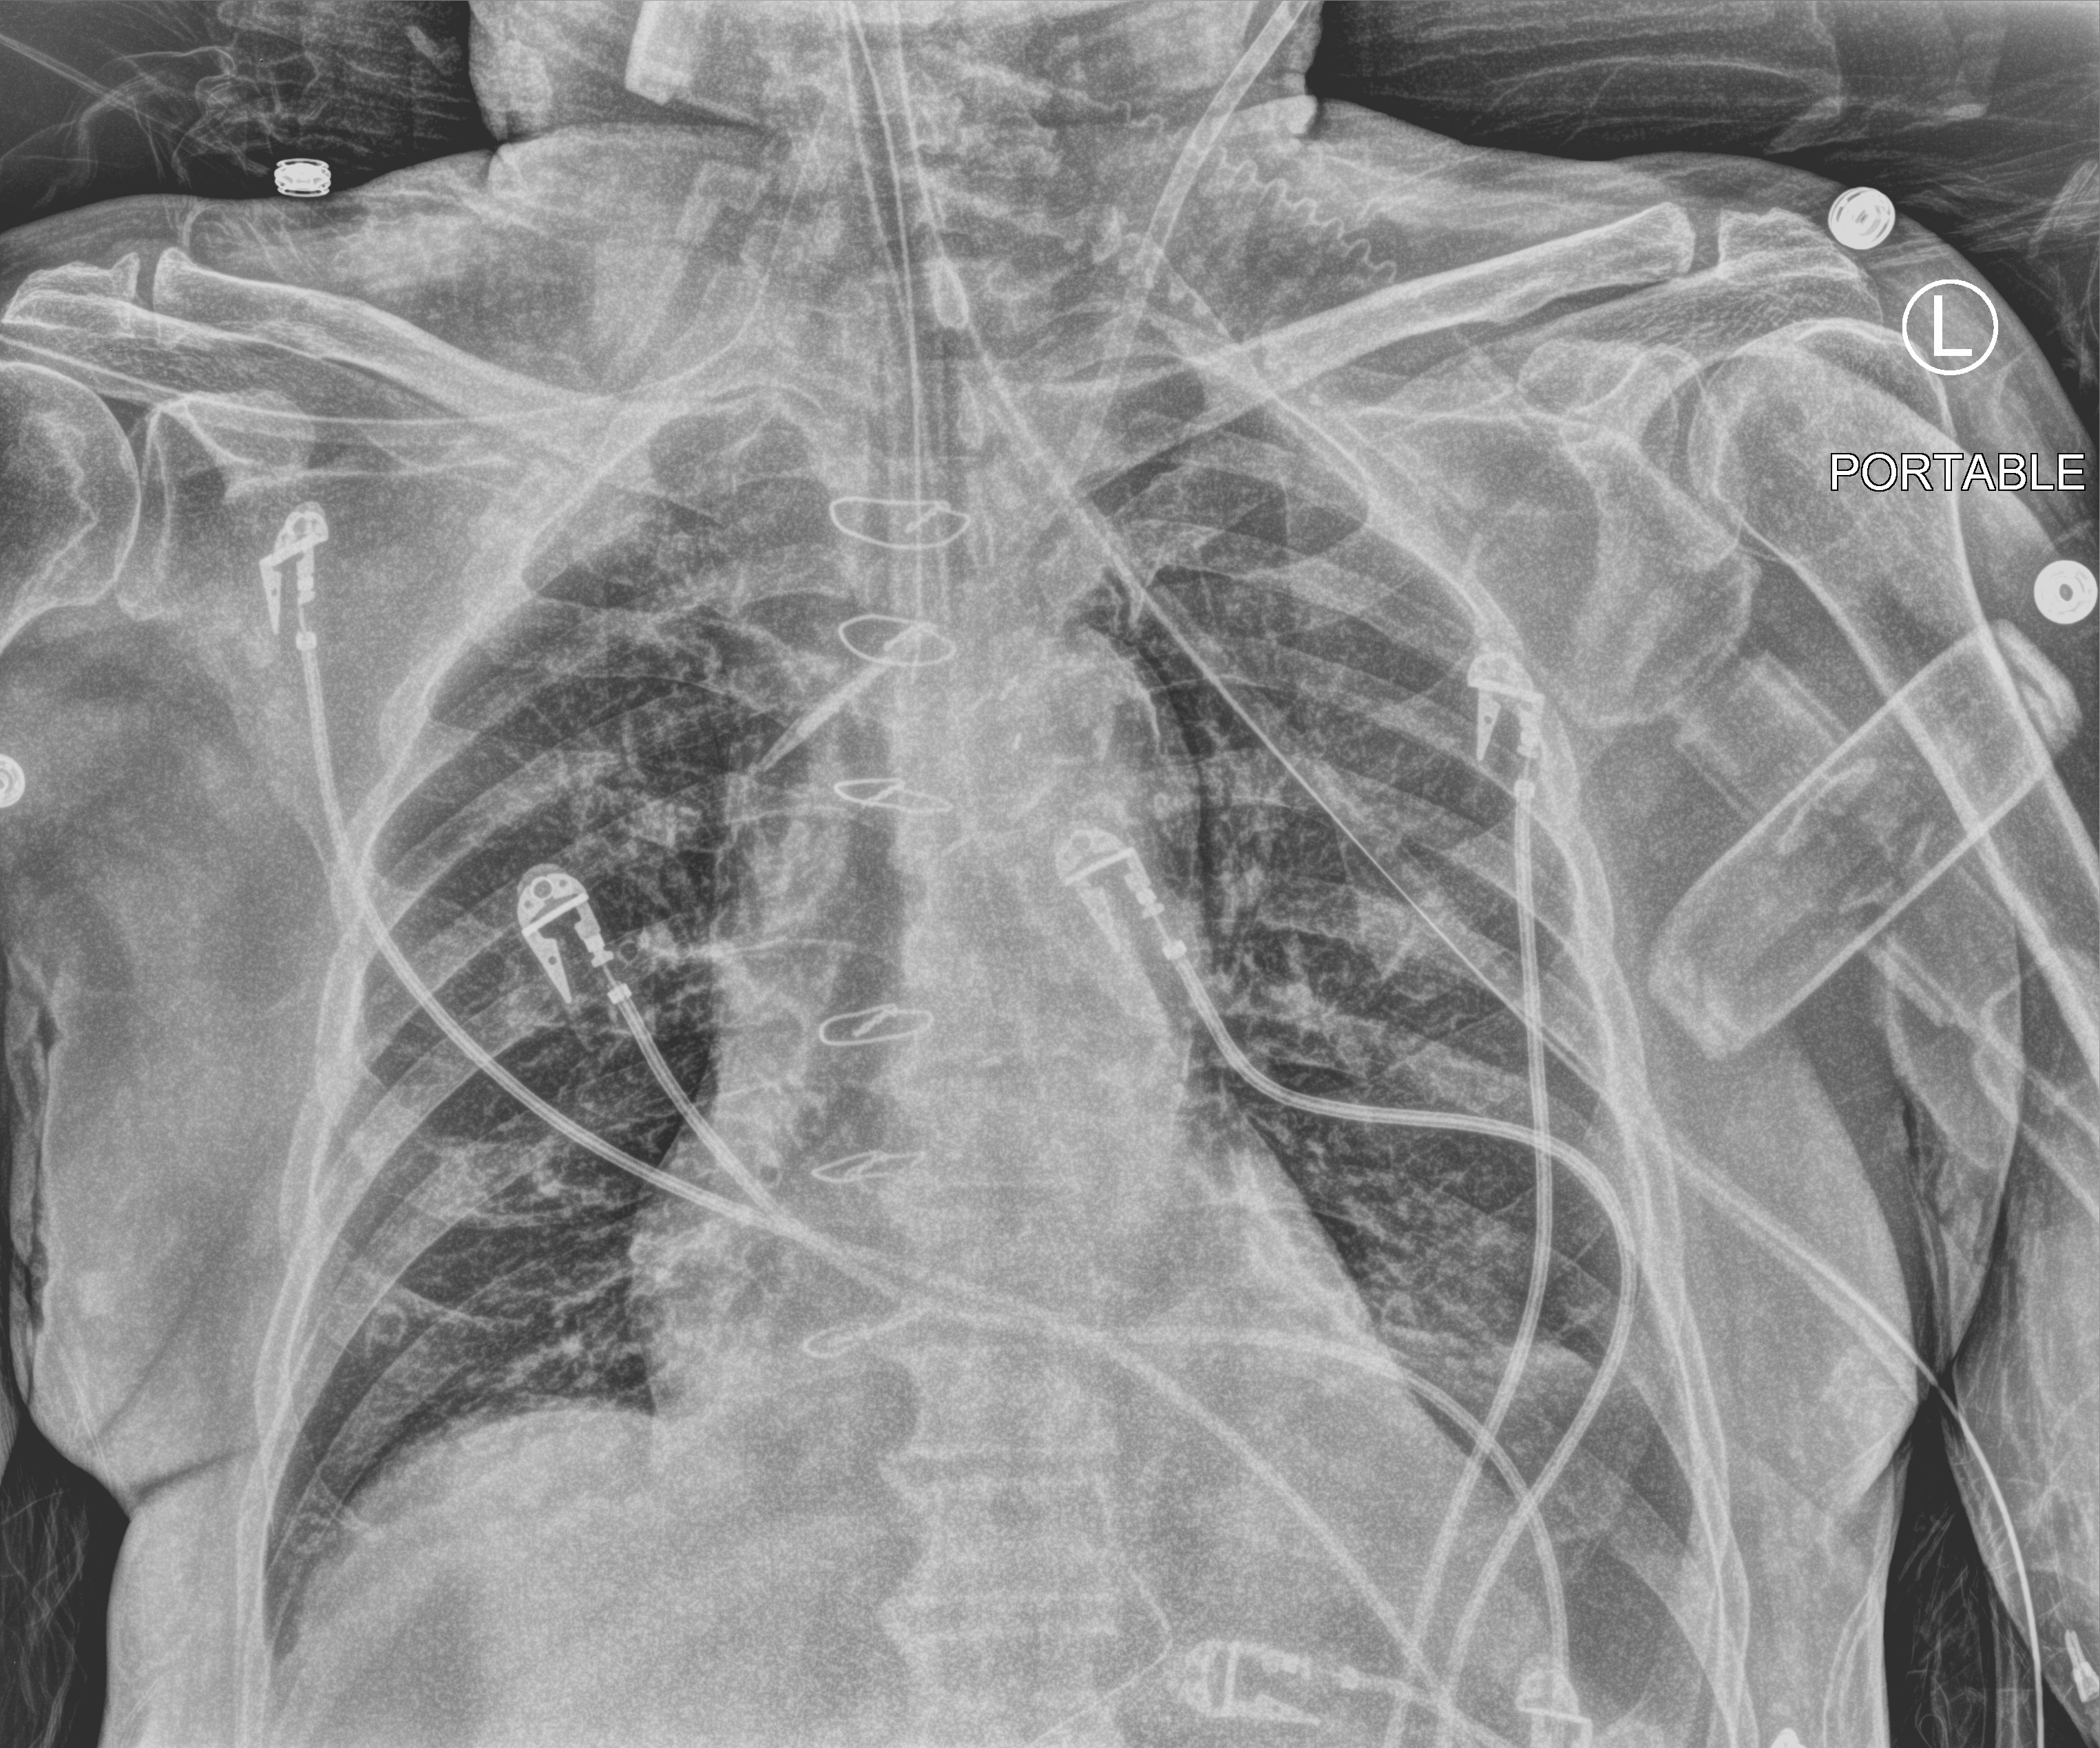
Bedside chest radiograph (computed radiography). Patient hospitalised with COVID-19; male, aged 75–90 years.
Hospital-stay facts (about this admission, not read from this image; timing relative to this image not recorded):
- mechanically ventilated during this hospital stay: yes
- admitted to intensive care during this hospital stay: yes
- hypertension (admission record): yes